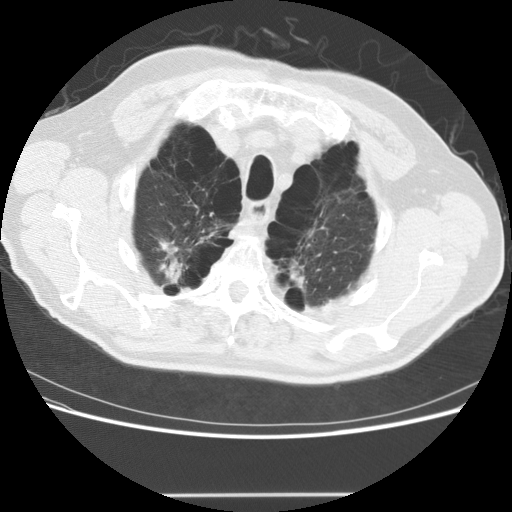
Low-dose screening chest CT, one axial slice; 120 kVp; lung window (W 1500 / L -600 HU); 2.5 mm slice thickness; 512 × 512 image matrix, field of view 360 × 360 mm.
Structures marked on this image (manually delineated by an expert):
- lesion 1 (tumor, upper lobe of right lung): box from (x=160, y=257) to (x=184, y=283) px